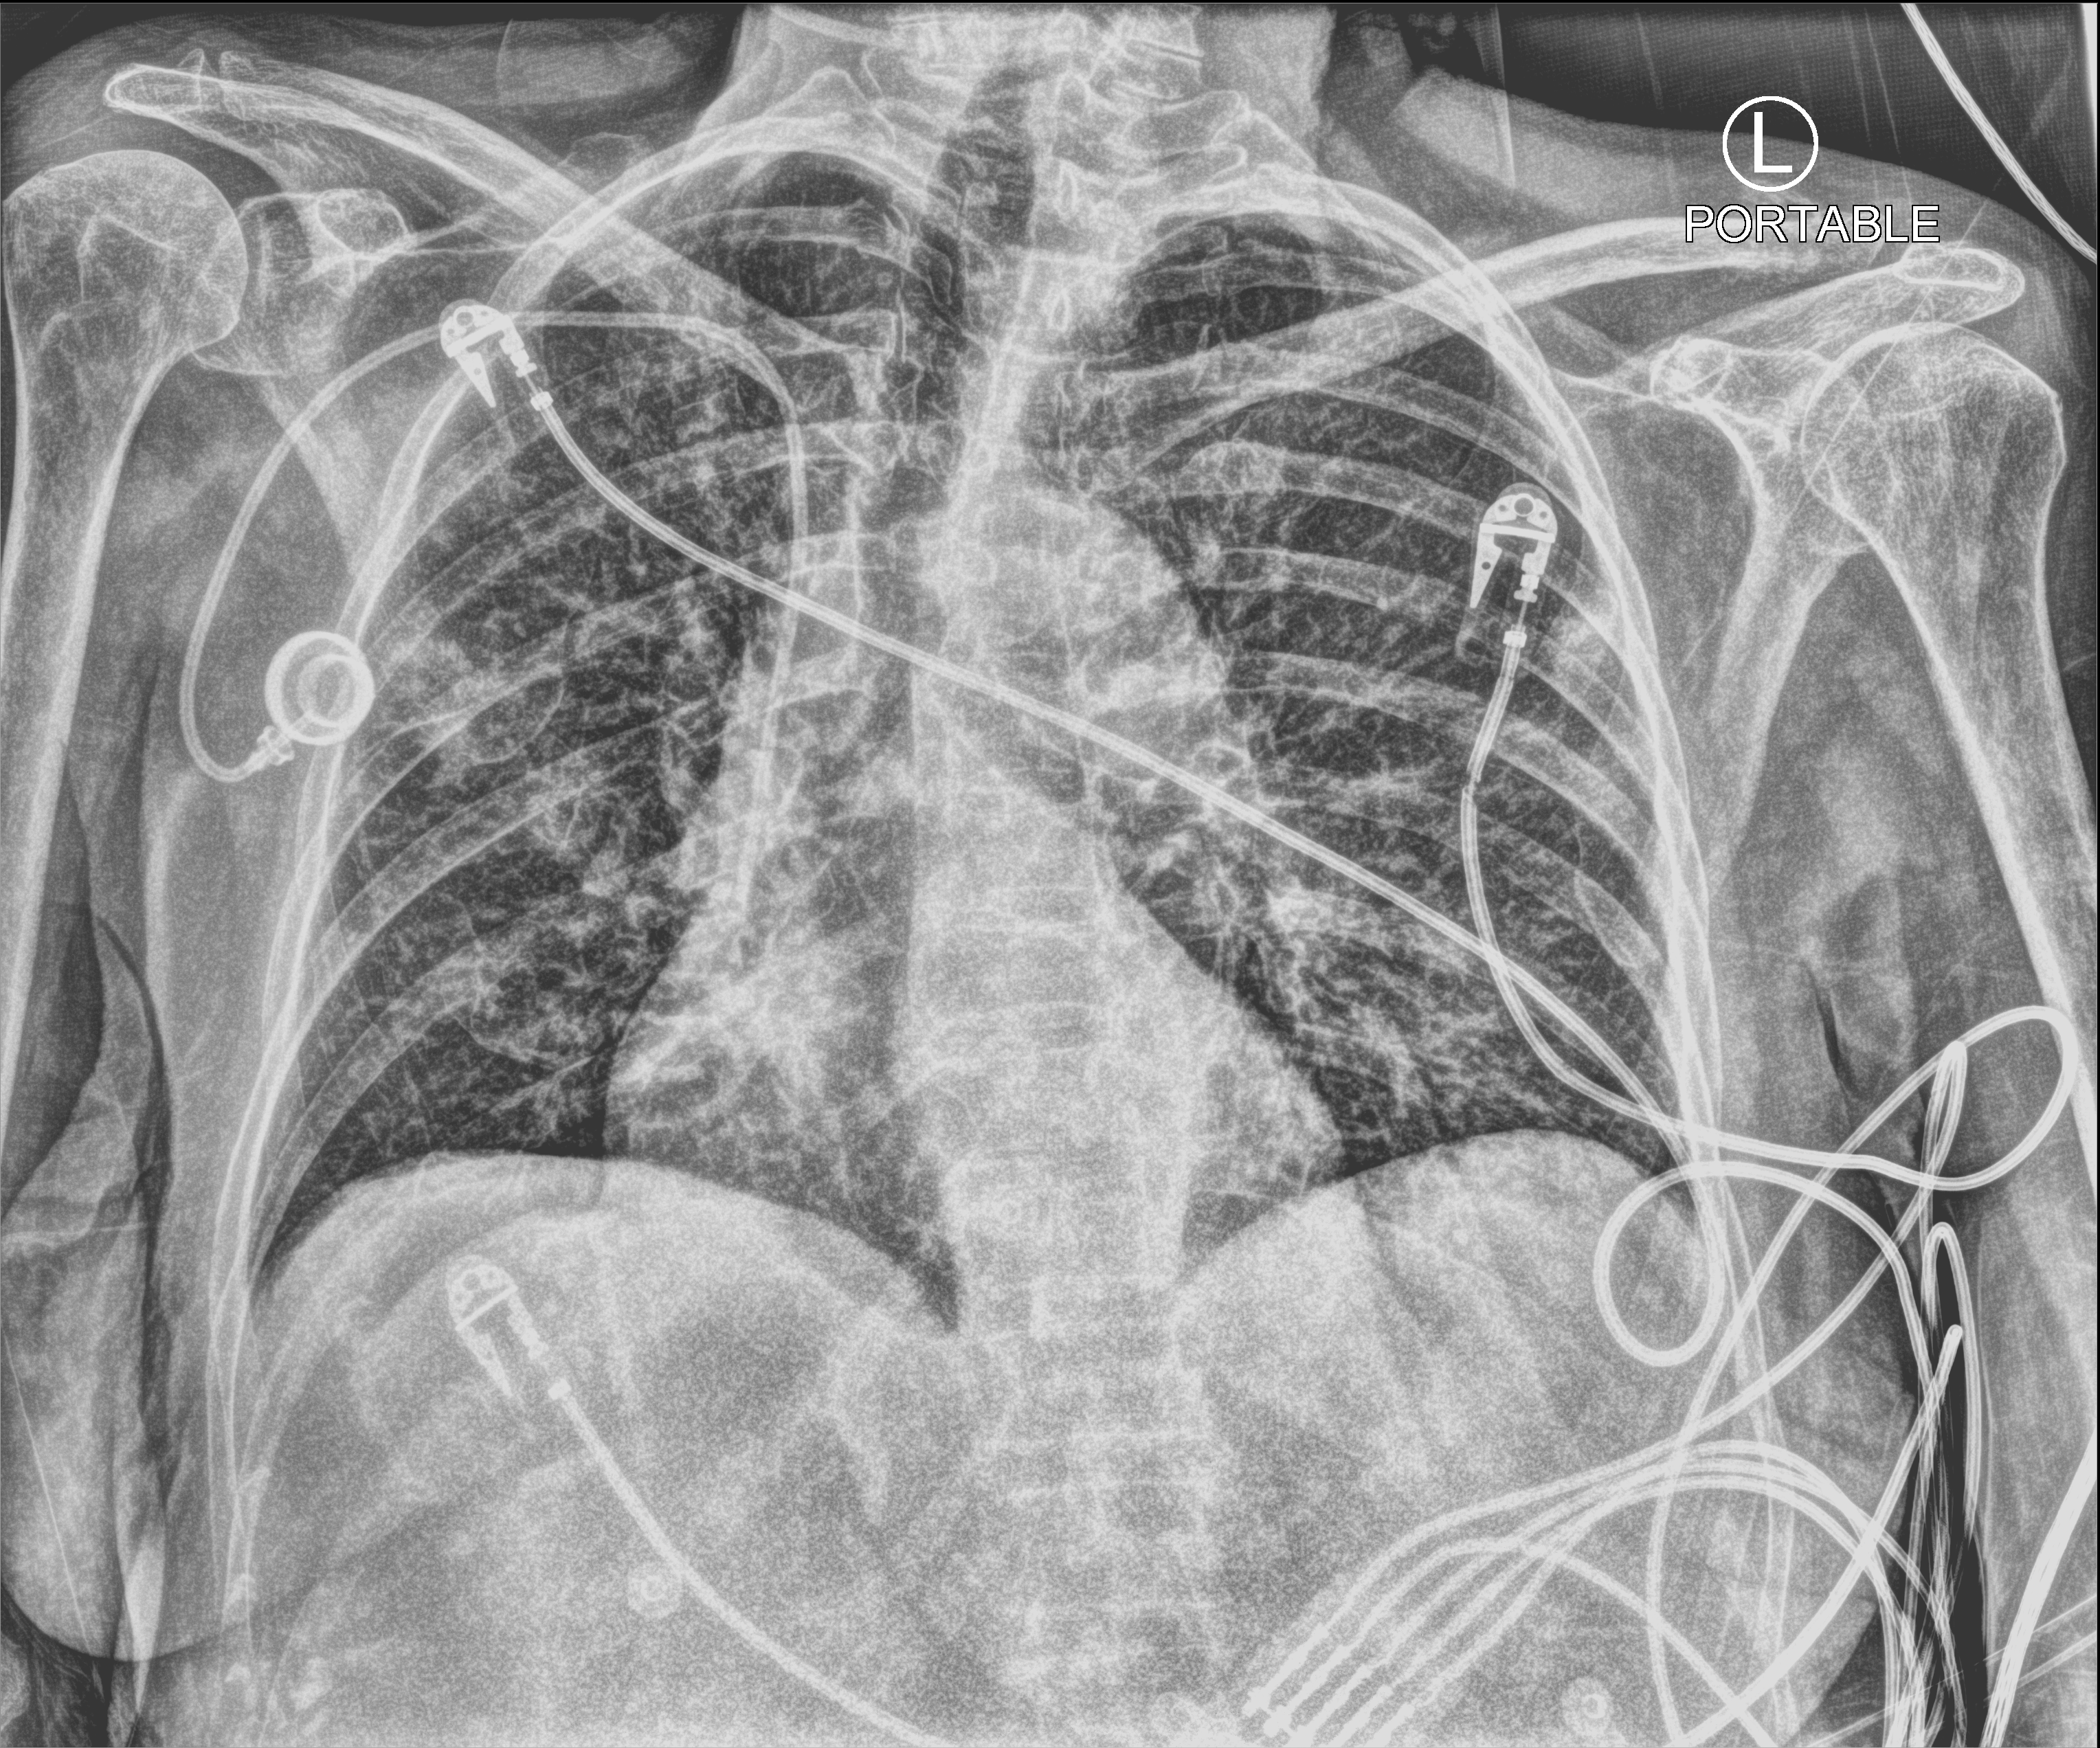
Chest X-ray (portable); anteroposterior (AP) projection. Female patient hospitalised with COVID-19, age 75–90 years.
Admission-level facts for this patient (not findings on this image; timing relative to this image not recorded):
- mechanically ventilated during this hospital stay: no
- admitted to intensive care during this hospital stay: yes